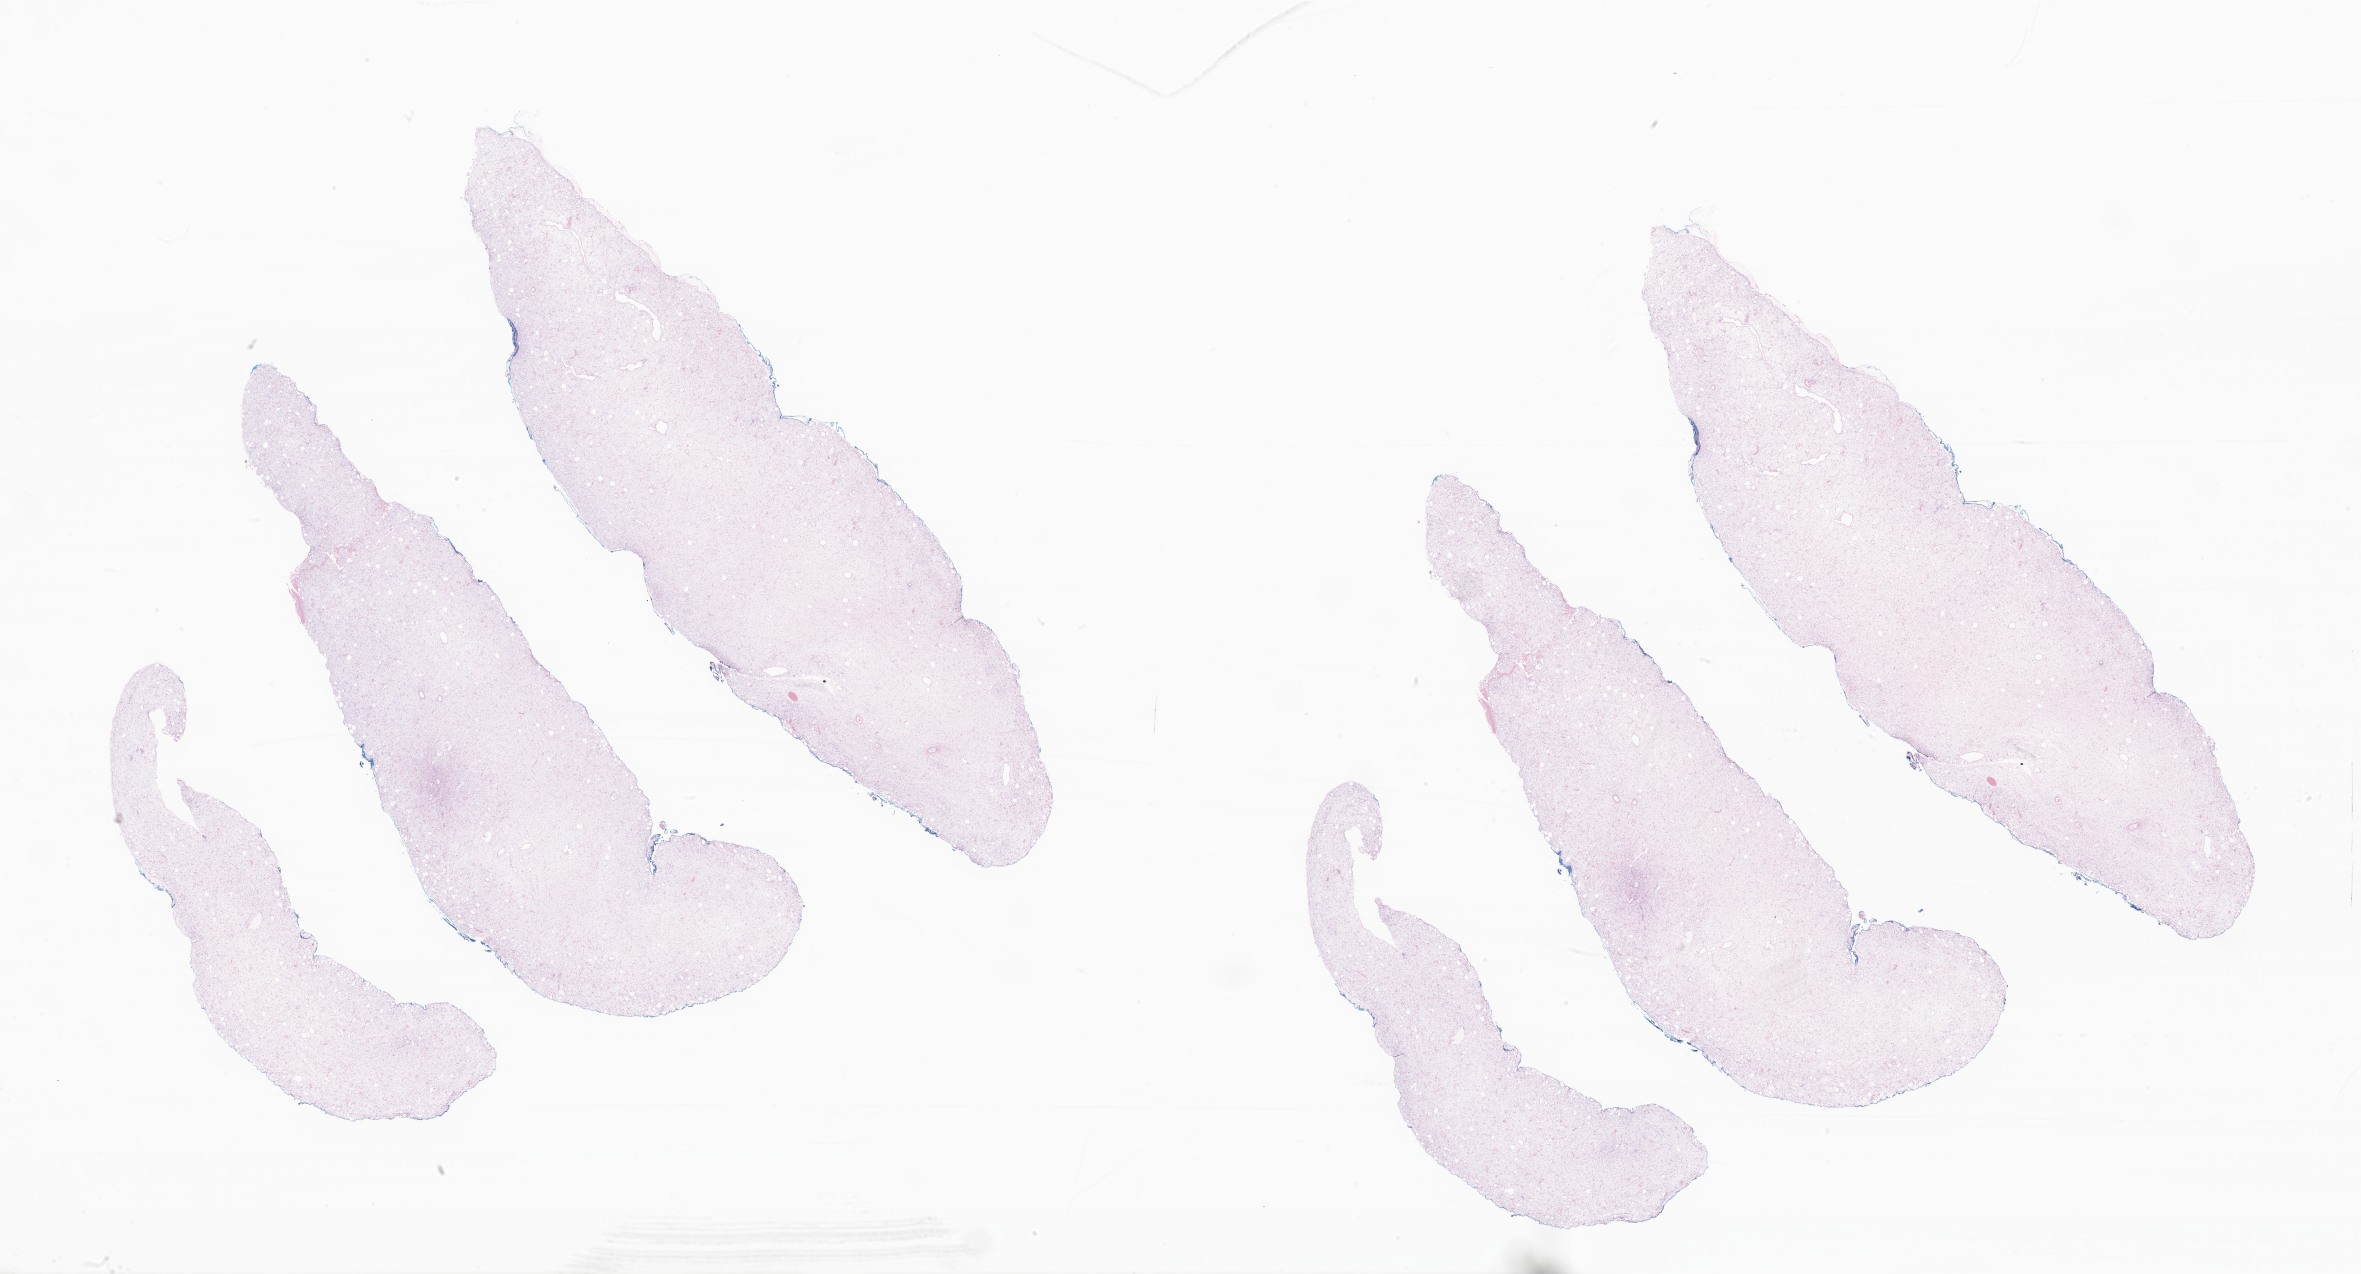
Digitized haematoxylin and eosin-stained section of tumor tissue from the abdomen, shown as a low-resolution overview of the whole scanned area (about 39.8 x 21.5 mm). FFPE section. Patient male; age 187 months (15 years 7 months).
Recorded diagnosis: Myxoid liposarcoma.